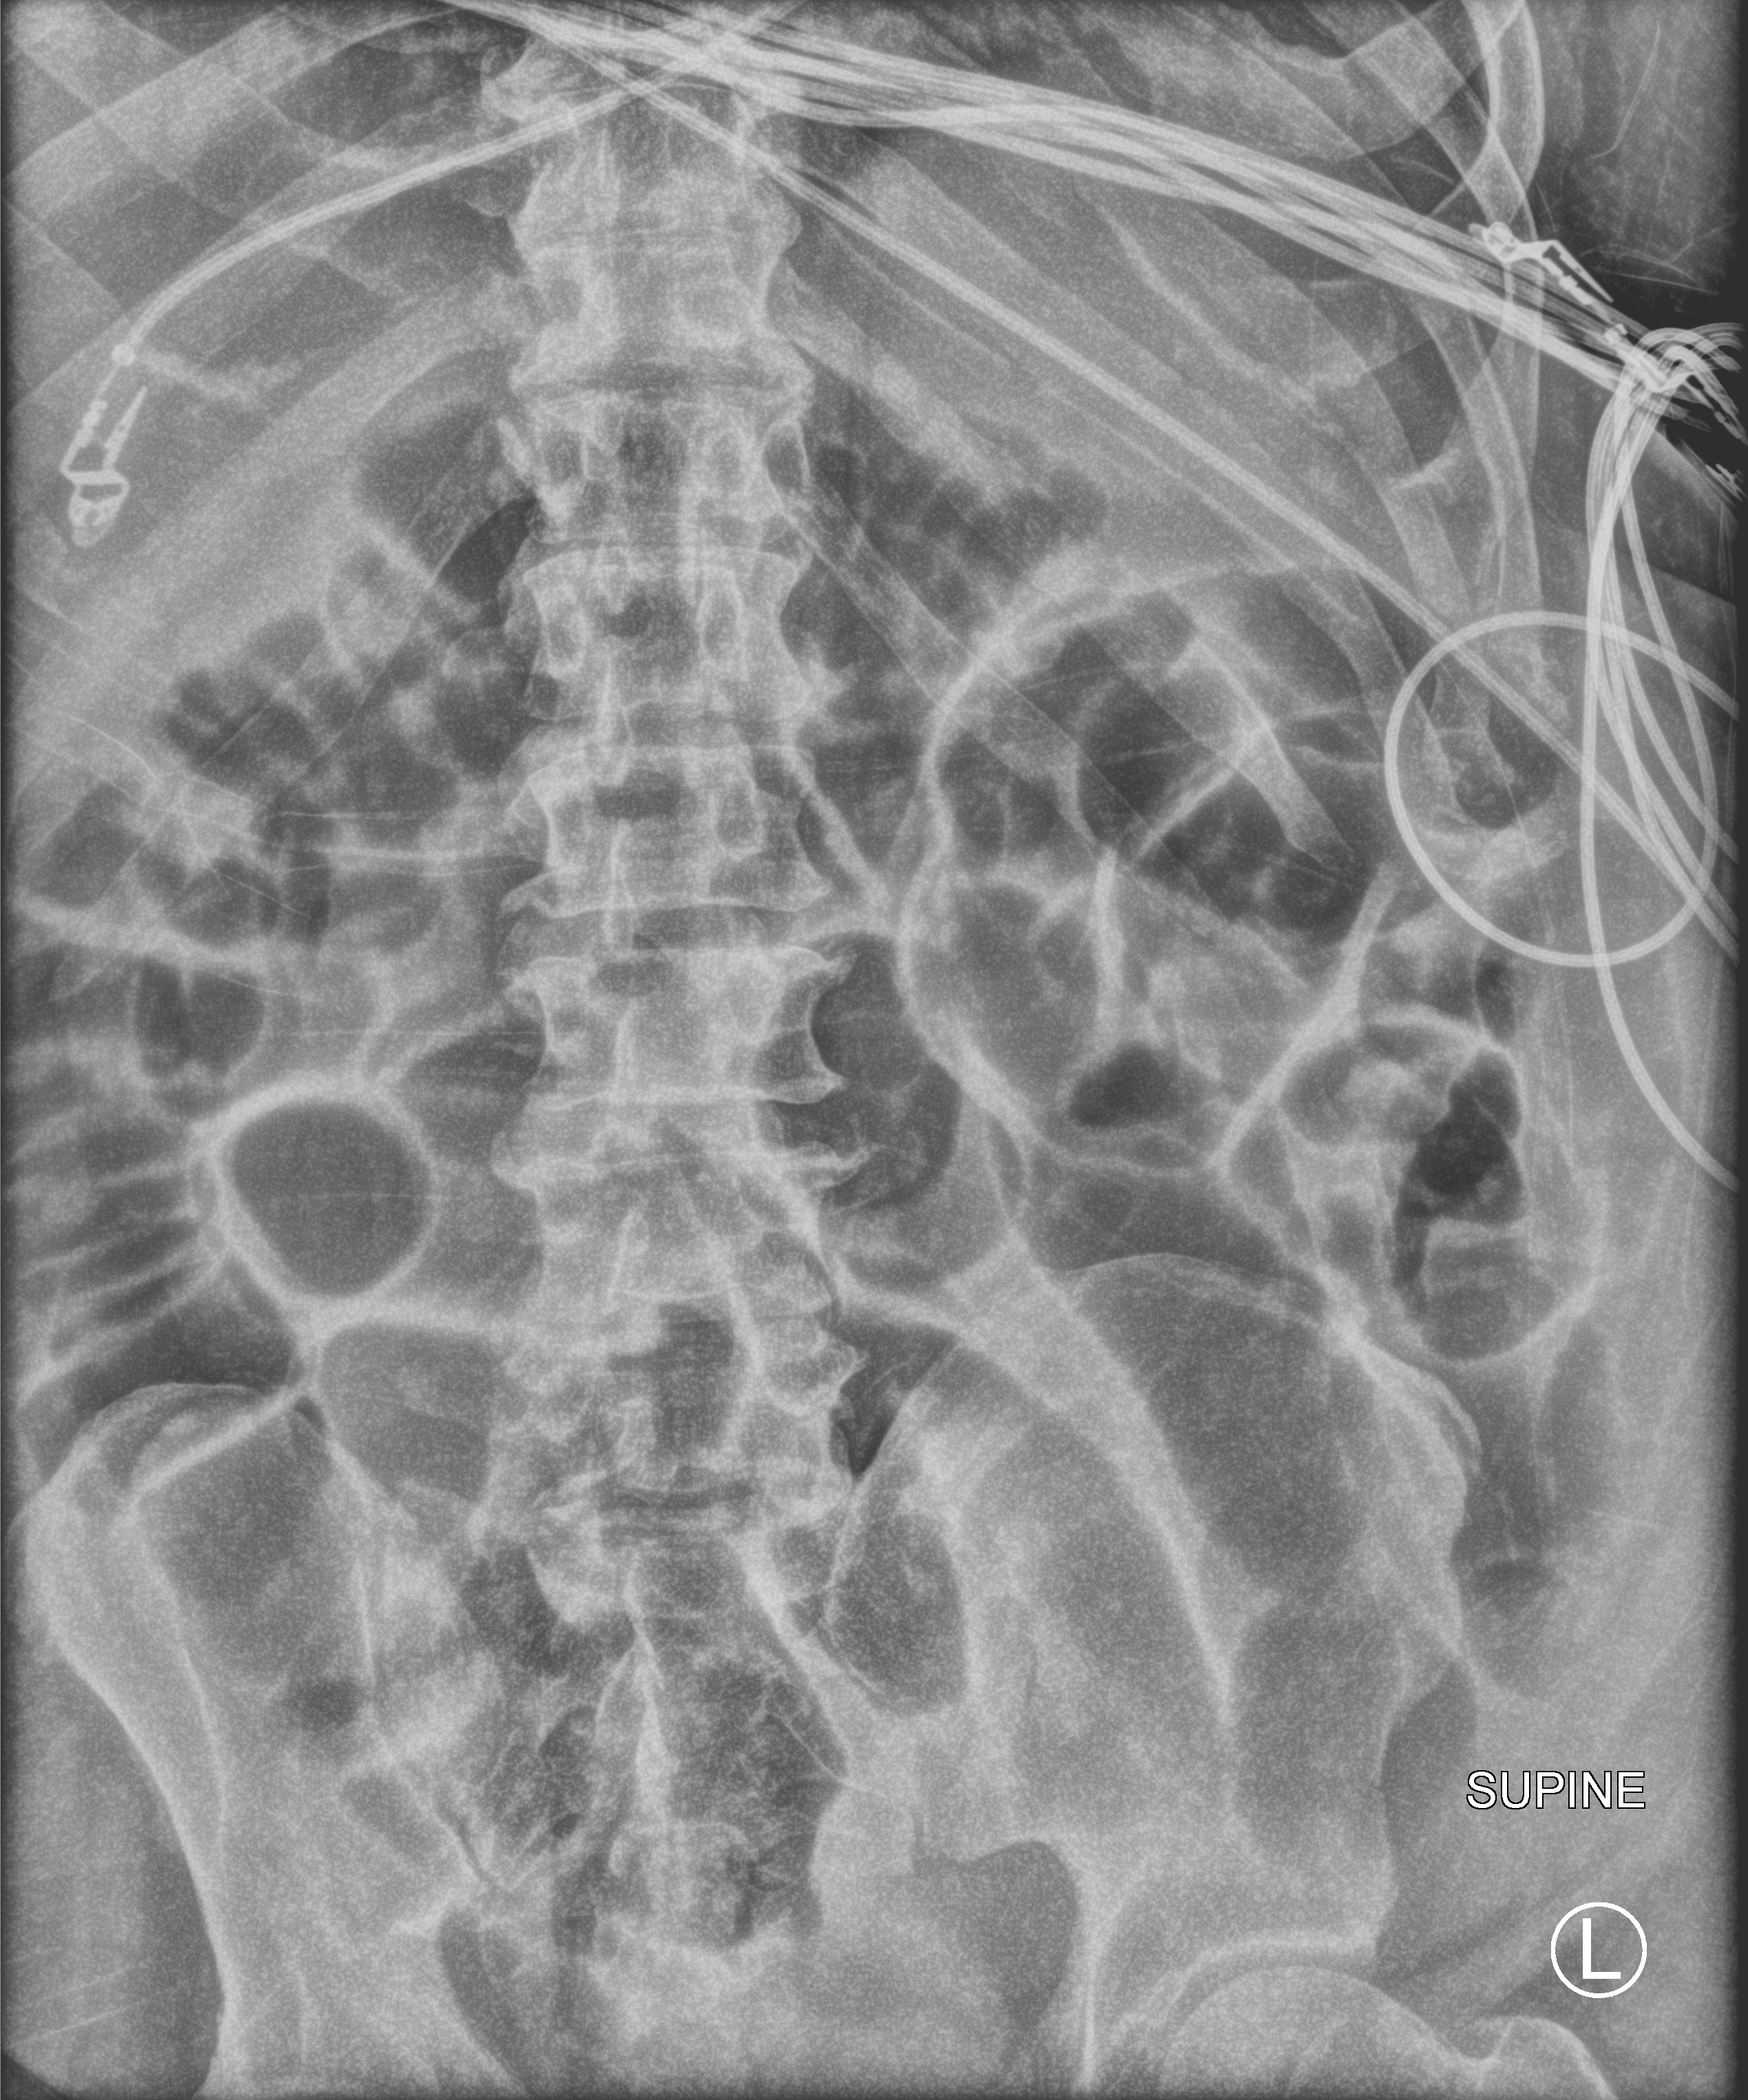
Abdomen X-ray (portable), anteroposterior (AP) projection. Male patient hospitalised with COVID-19, age 18–59 years.
From the hospital-stay record, not from the radiograph (when in the stay this image was taken is not recorded): smoking status (admission record): never.